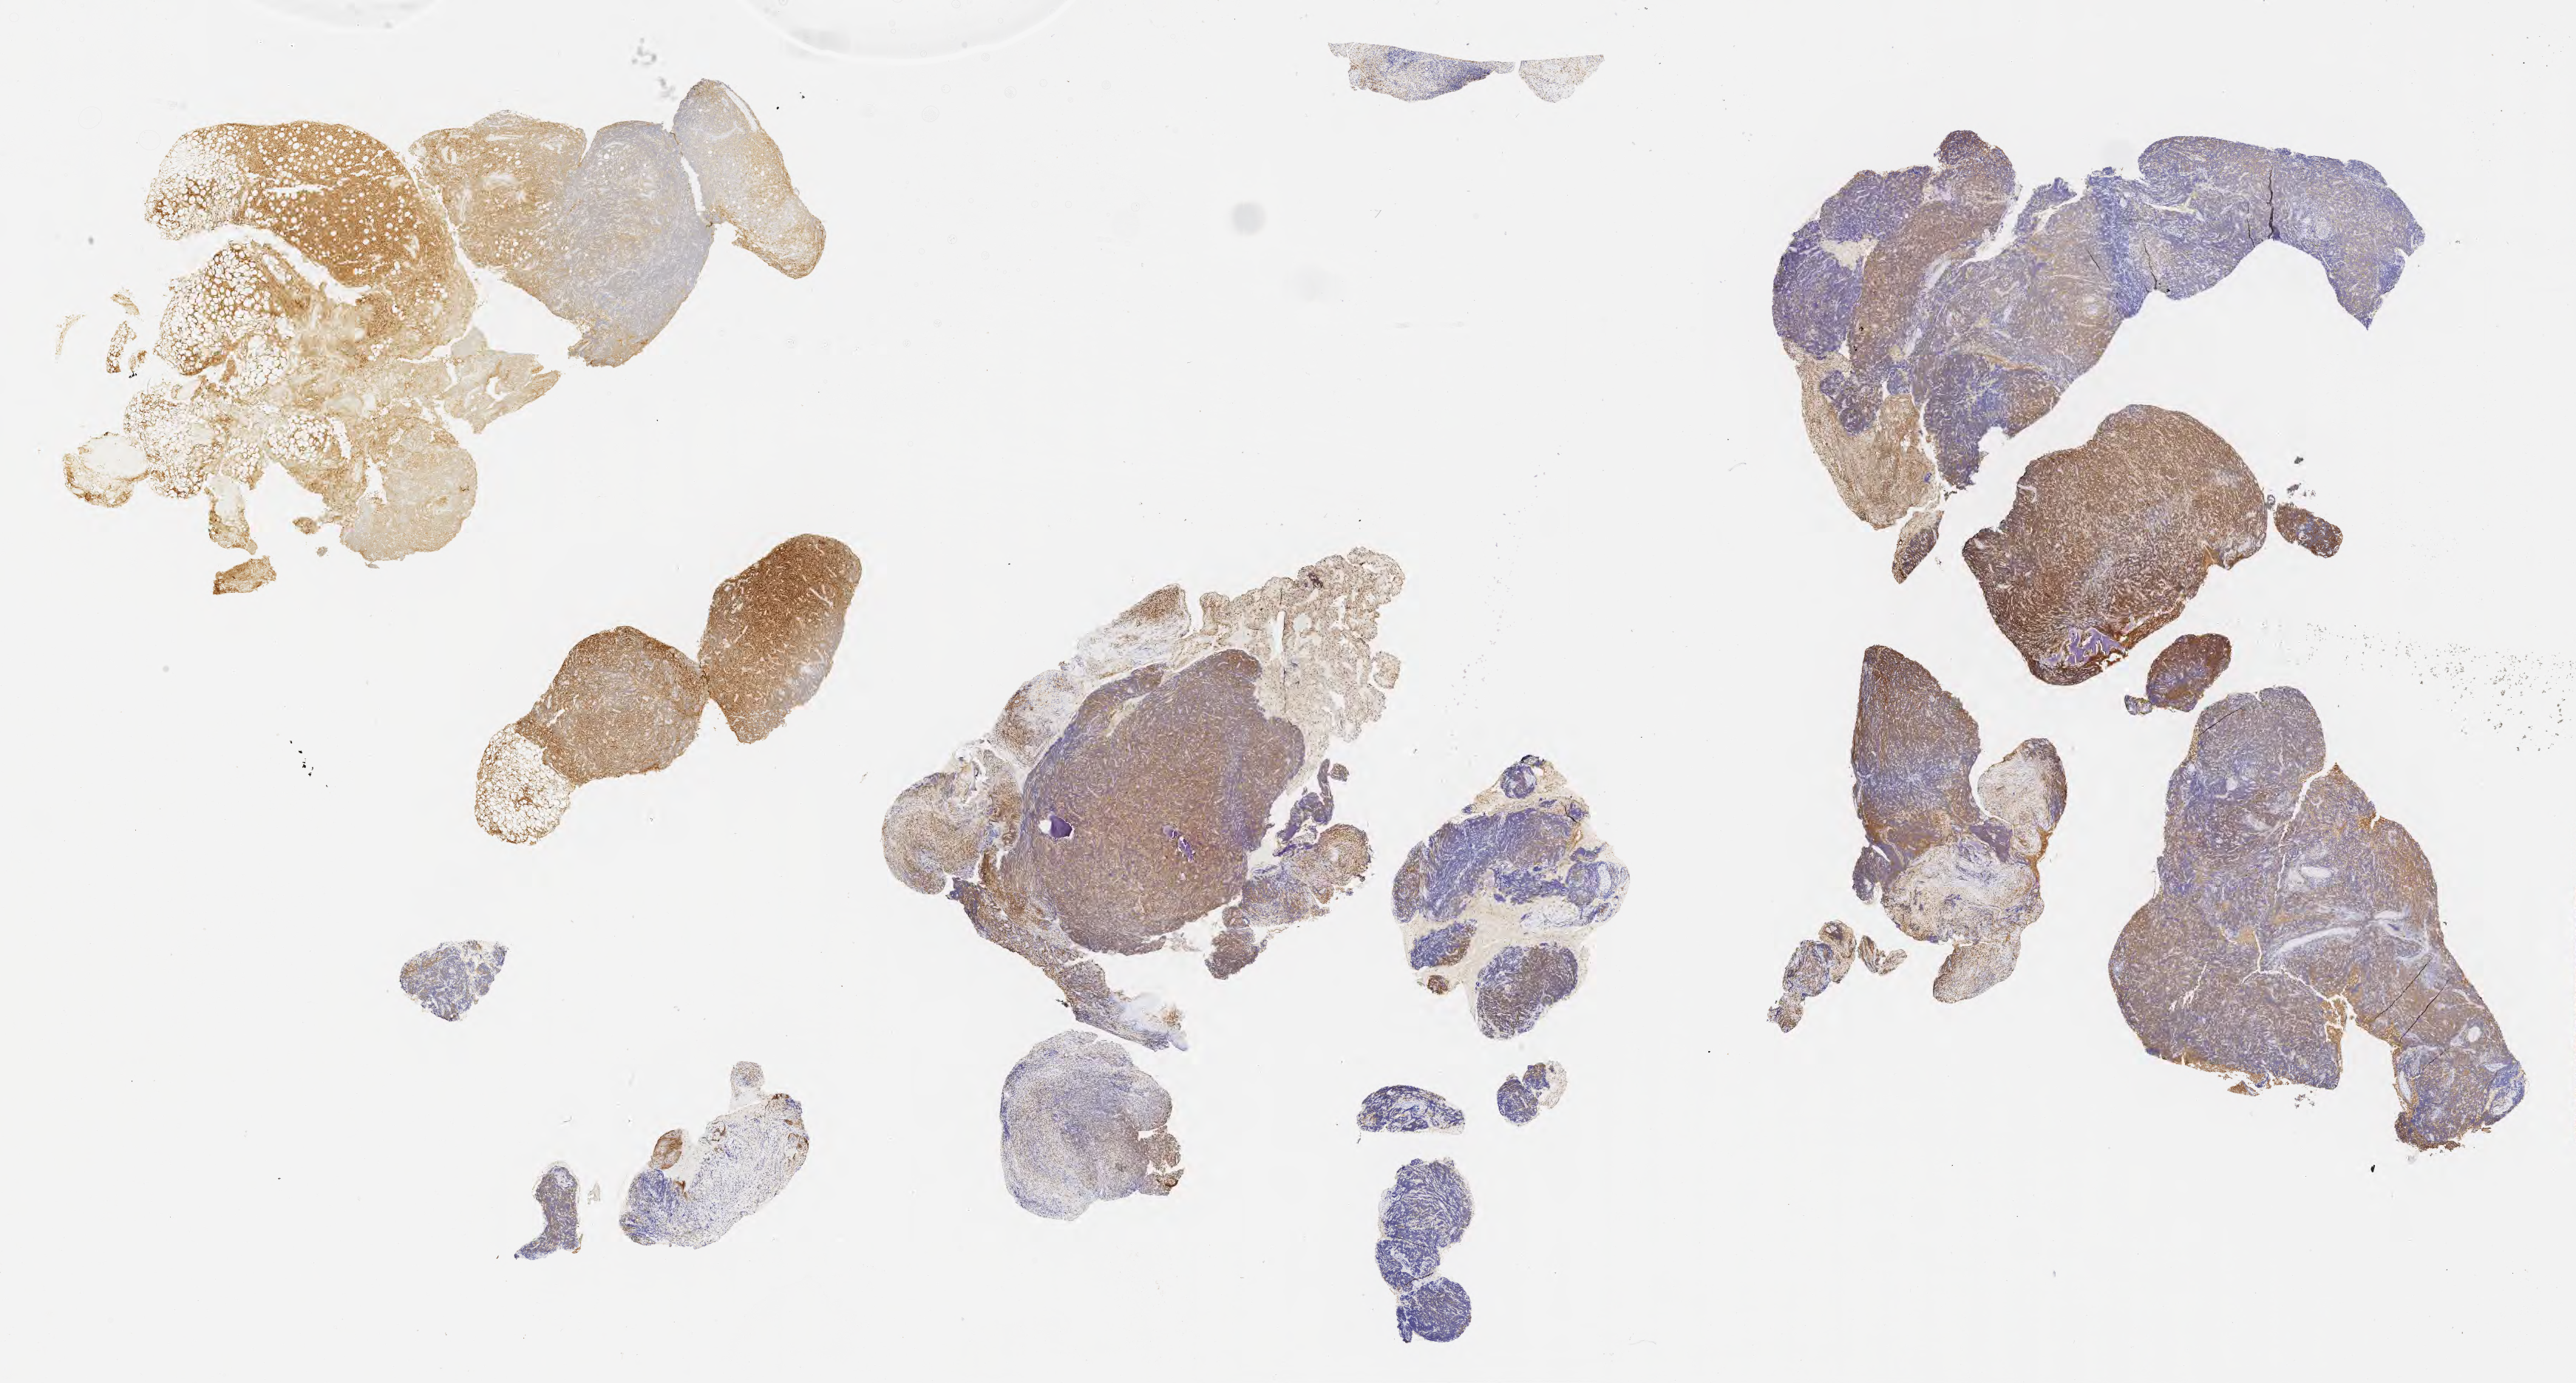
Immunohistochemistry (IHC) whole-slide image stained for CD10, low-resolution overview of the scanned area, about 28.2 x 15.1 mm. Specimen: tumor tissue. Patient: male, age 45 years.
Diagnosis: Diffuse large B-cell lymphoma, NOS.